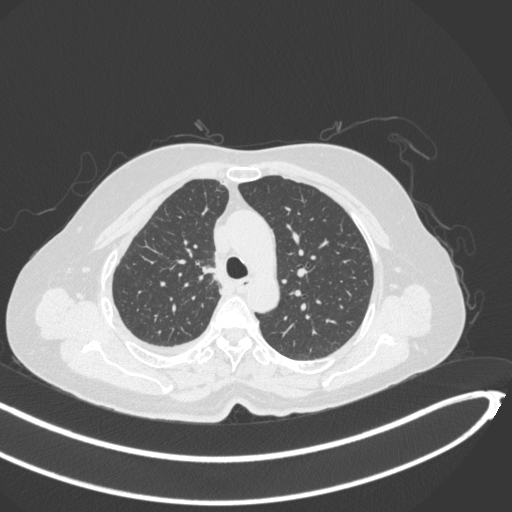
Chest CT, one axial slice; position 217 of 297 along the scan axis; reconstruction kernel B31f; lung window (W 1500 / L -600 HU); 512 × 512 image matrix, field of view 400 × 400 mm. Patient: female, 64 years. Case-level facts recorded for this patient, not image findings: clinical TNM (as recorded): T1b N0 M1.
Structures marked on this image (rectangle marked by the reading radiologist):
- lung tumour (recorded histology: adenocarcinoma): bounding box <196,256,218,287> (left, top, right, bottom; pixels)